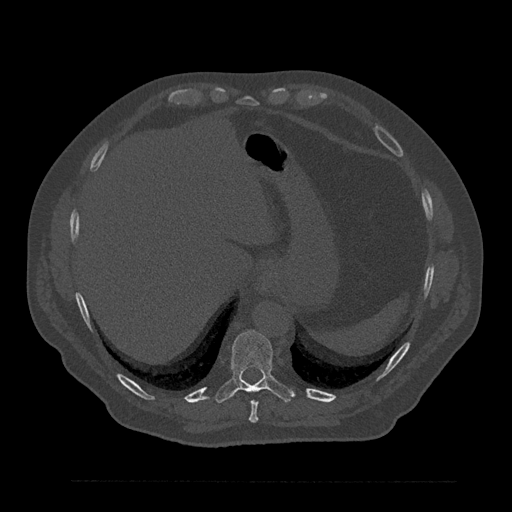
CT including the spine, one axial slice; position 361 of 797 along the scan axis; 120 kVp; bone window (W 1800 / L 400 HU); 0.5 mm slice thickness; 512 × 512 image matrix, field of view 430 × 430 mm. Male patient, age 61 years. From the clinical record (not read from this slice): primary cancer: prostate.
Outlined on this slice (semi-automatically segmented with operator editing):
- T10 vertebra: bounding box (x1, y1, x2, y2) in pixels: (216, 330, 295, 403)
- T9 vertebra: (249, 400, 258, 423)